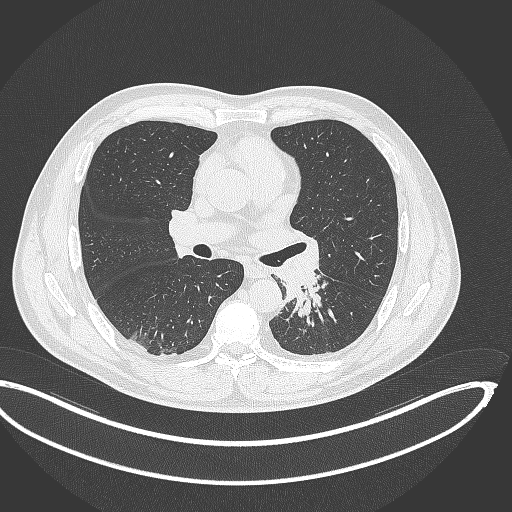
Chest CT, one axial slice; slice 199 of 362 in the series (ordered by position); 120 kVp; lung window (W 1500 / L -600 HU); 1 mm slice thickness; 512 × 512 image matrix, field of view 442 × 442 mm. Male patient, age 50 years. Case-level facts recorded for this patient, not image findings: clinical TNM (as recorded): T2a N3 M0.
Structures marked on this image (bounding box drawn by a radiologist):
- lung tumour (recorded histology: squamous cell carcinoma): box from (x=280, y=268) to (x=324, y=319) px